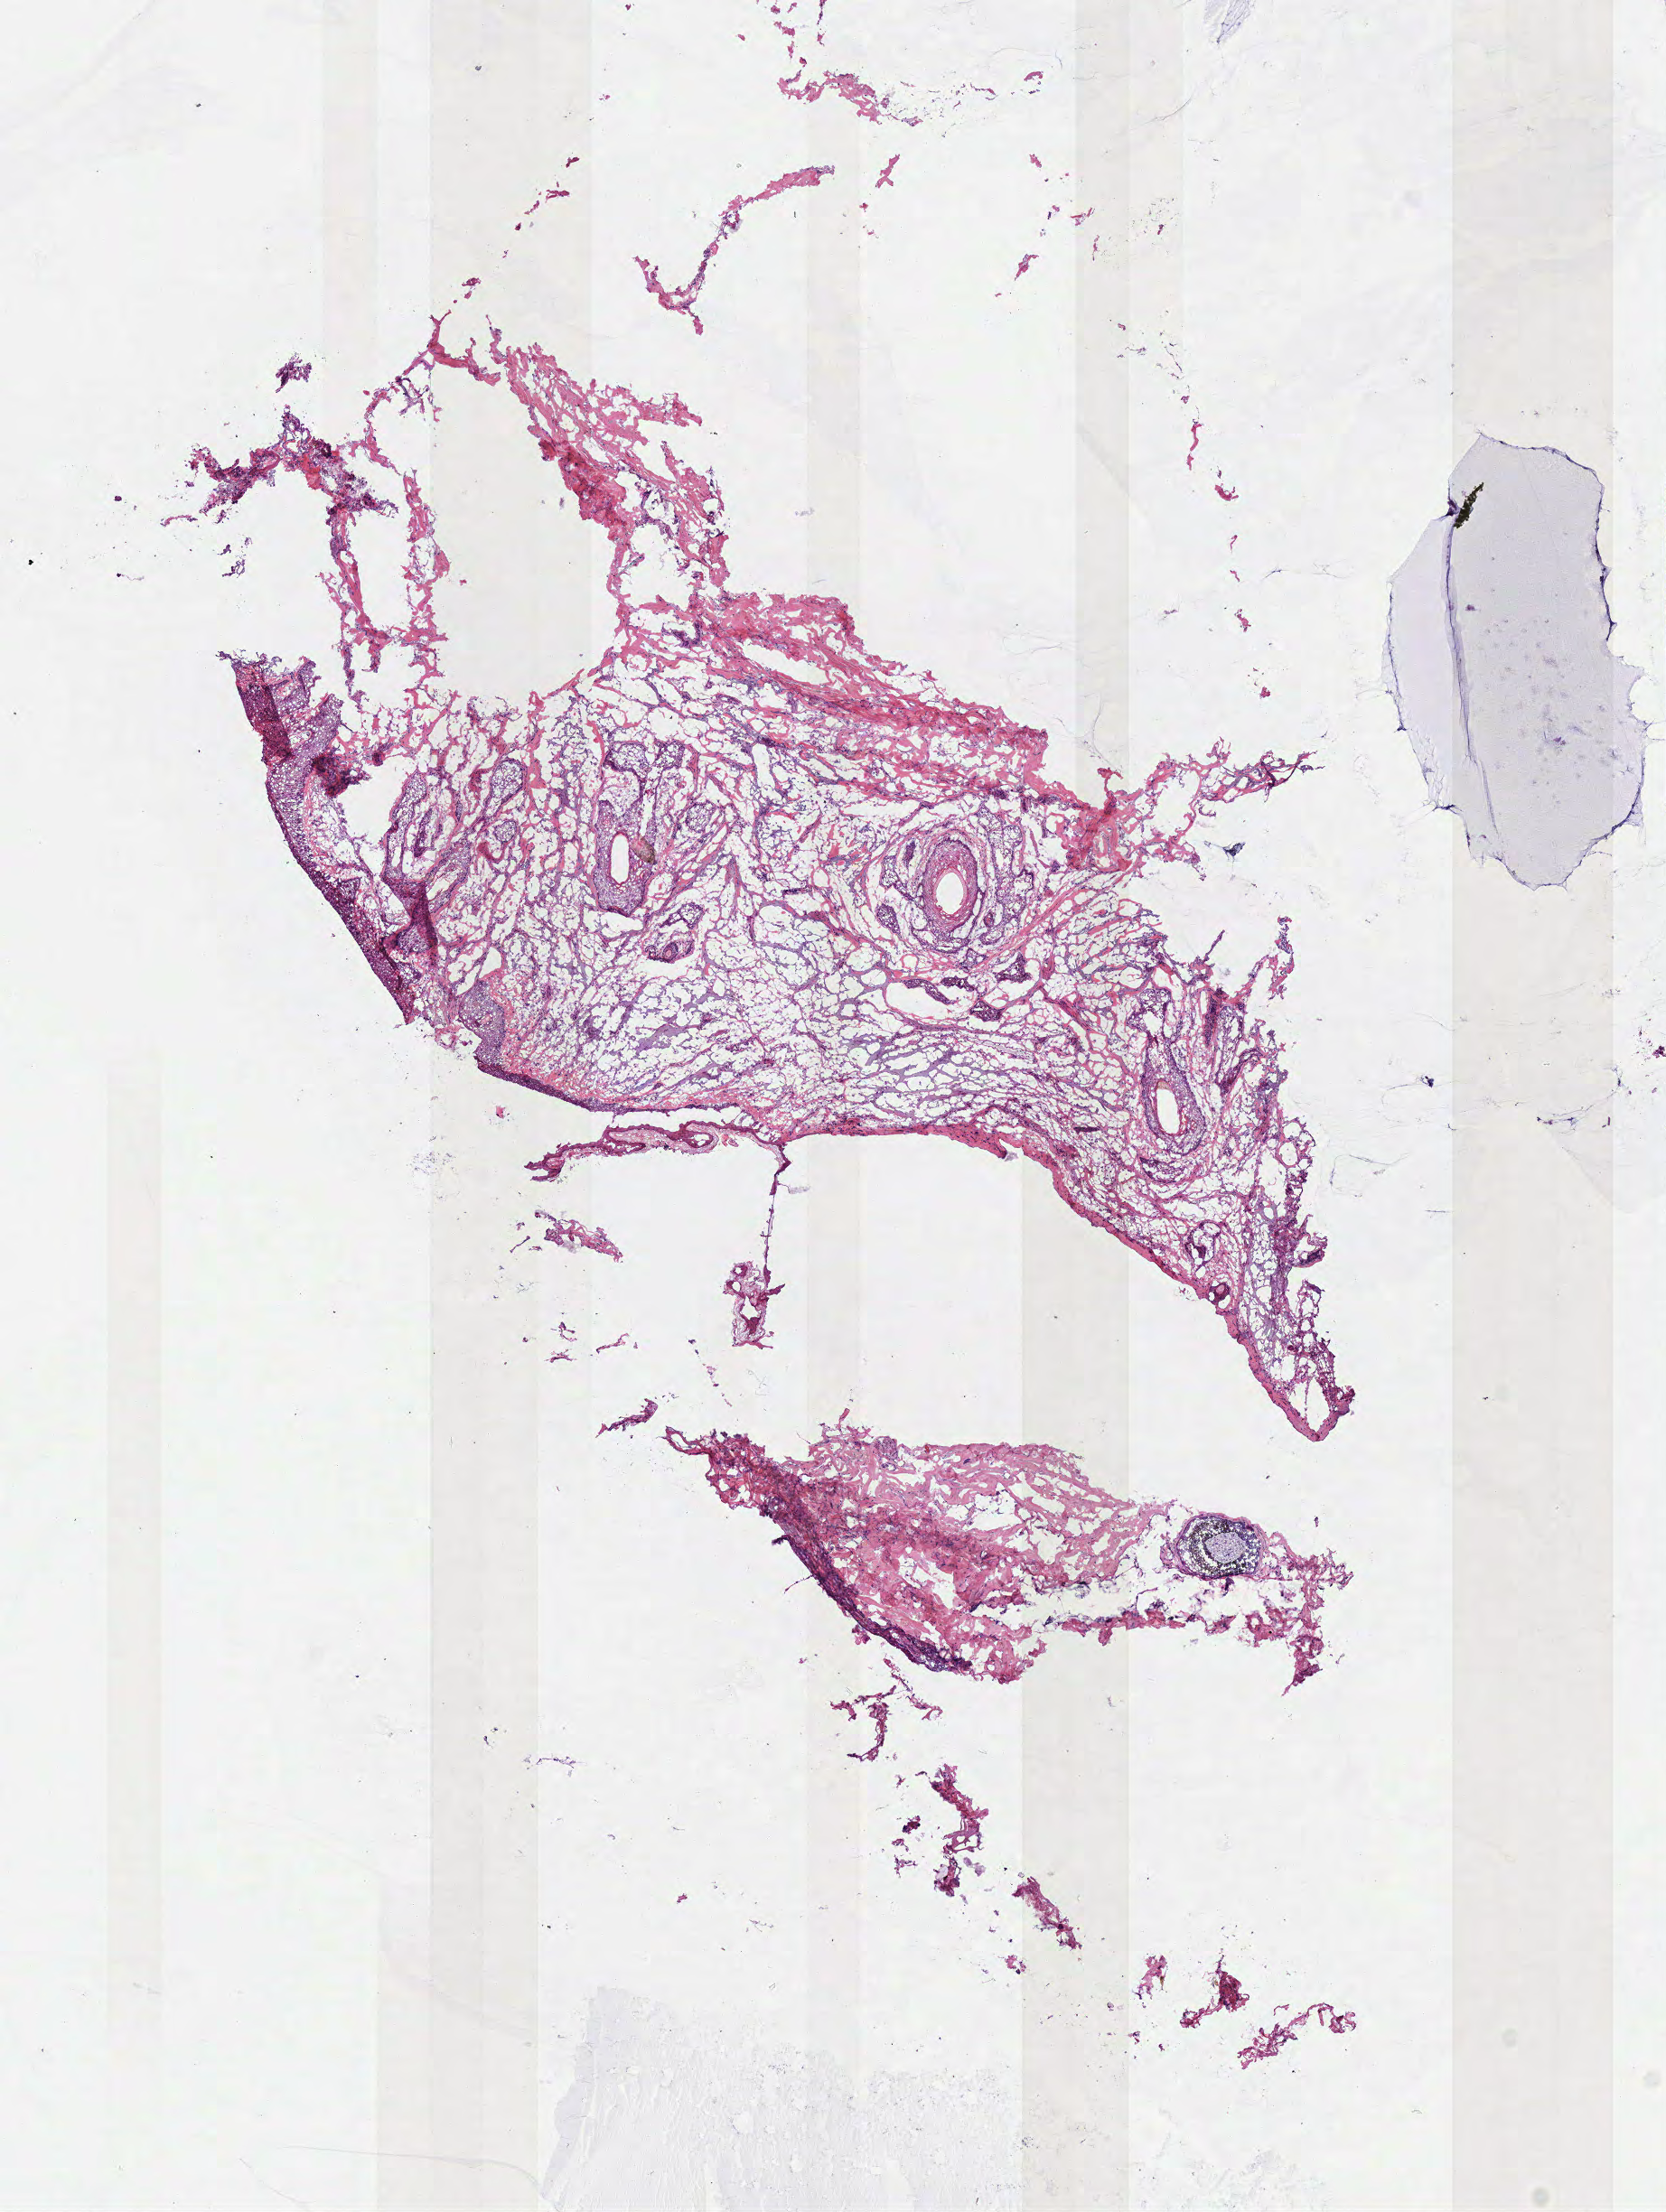
Whole-slide histology image, Hematoxylin and eosin (H&E) stained — shown as a low-resolution overview of the whole scanned area (about 7.3 x 9.6 mm). Frozen section from the top of the tissue portion. Solid tissue normal (non-tumour tissue) sample from the head and neck. Patient: male, age at initial diagnosis 87 years.
This section: solid tissue normal sample (biorepository sample class). Patient diagnosis: Squamous cell carcinoma, NOS (overlapping lesion of lip, oral cavity and pharynx).